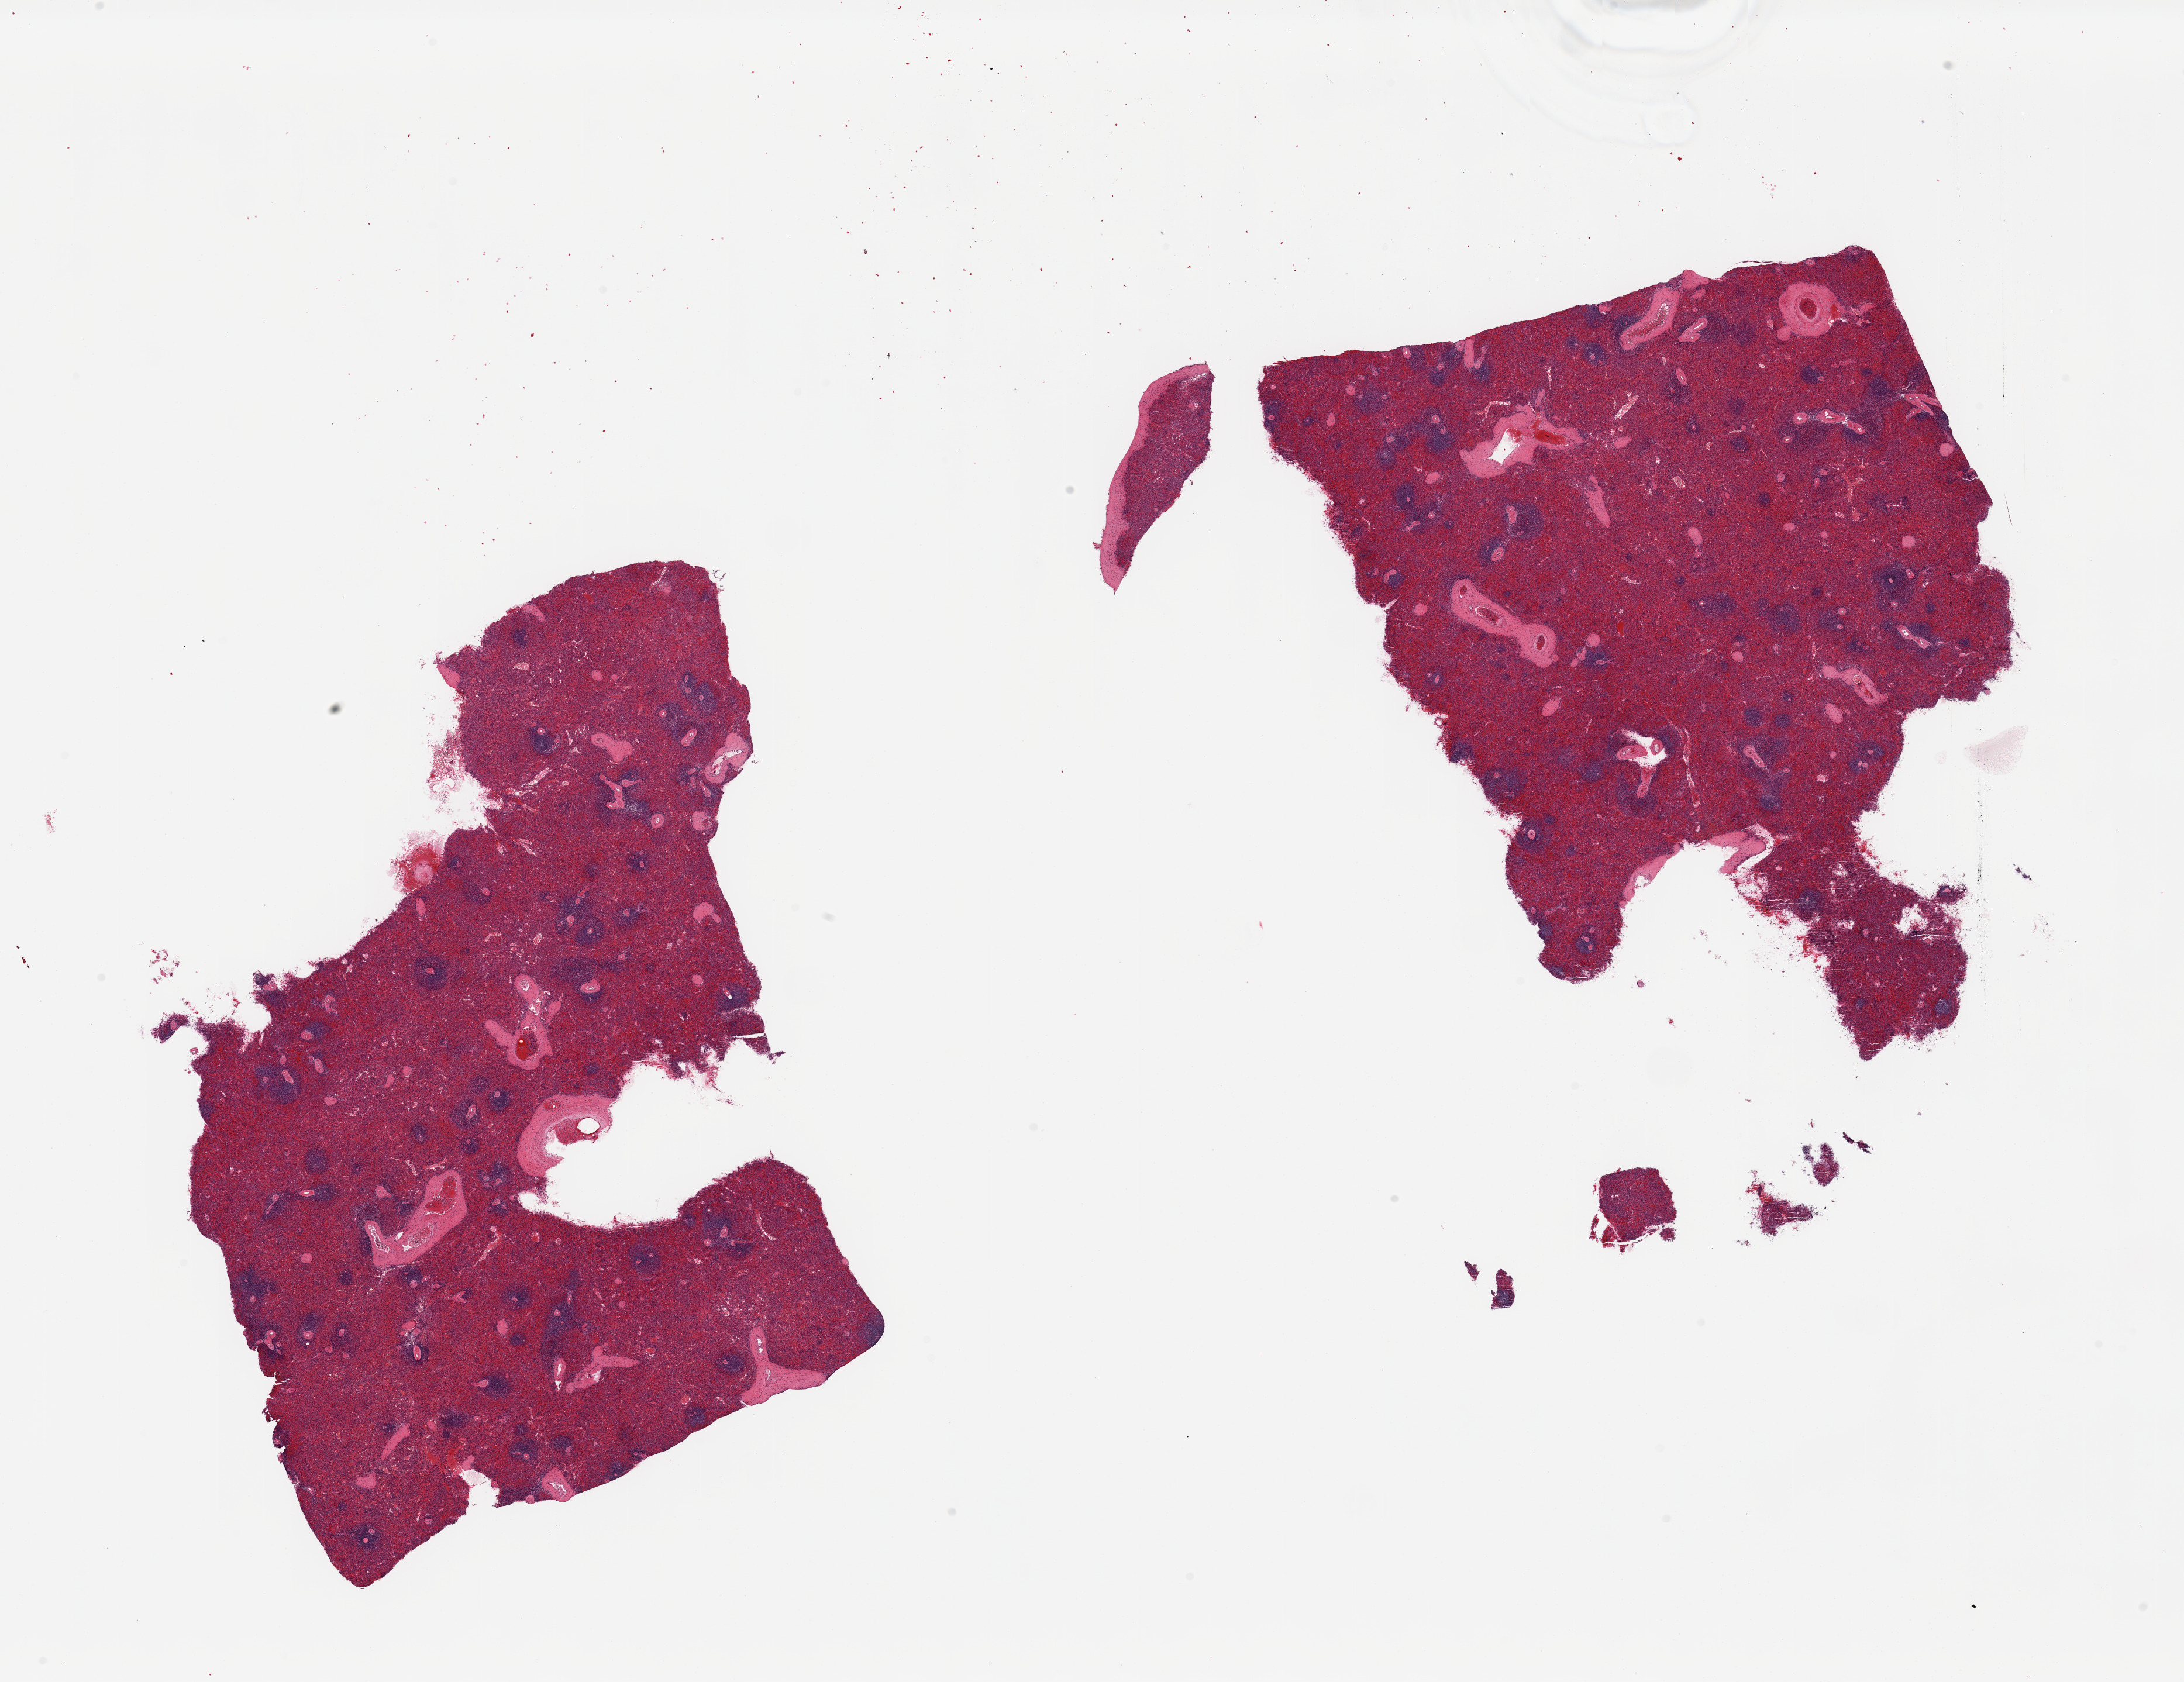
Hematoxylin and eosin (H&E) whole-slide image — low-resolution overview of the scanned area, about 29.5 x 22.7 mm, PAXgene-fixed, paraffin-embedded tissue, sampled site (target tissue): spleen, tissue donor sample. Donor: female.
Review note (as recorded): 2 pieces, mild congestion.